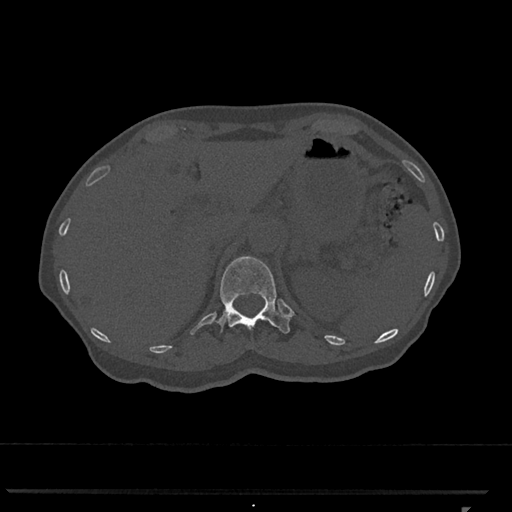
CT including the spine, one axial slice. Slice 463 of 793 in the series (ordered by position). Reconstruction kernel Br40s/3. 120 kVp. Bone window (W 1800 / L 400 HU). 0.5 mm slice thickness. 512 × 512 image matrix, field of view 380 × 380 mm. Patient: female, 62 years. Case-level facts recorded for this patient, not image findings: primary cancer: renal.
Structures marked on this image (semi-automatically segmented with operator editing):
- T12 vertebra: bounding box [x1, y1, x2, y2] px = [213, 256, 290, 334]